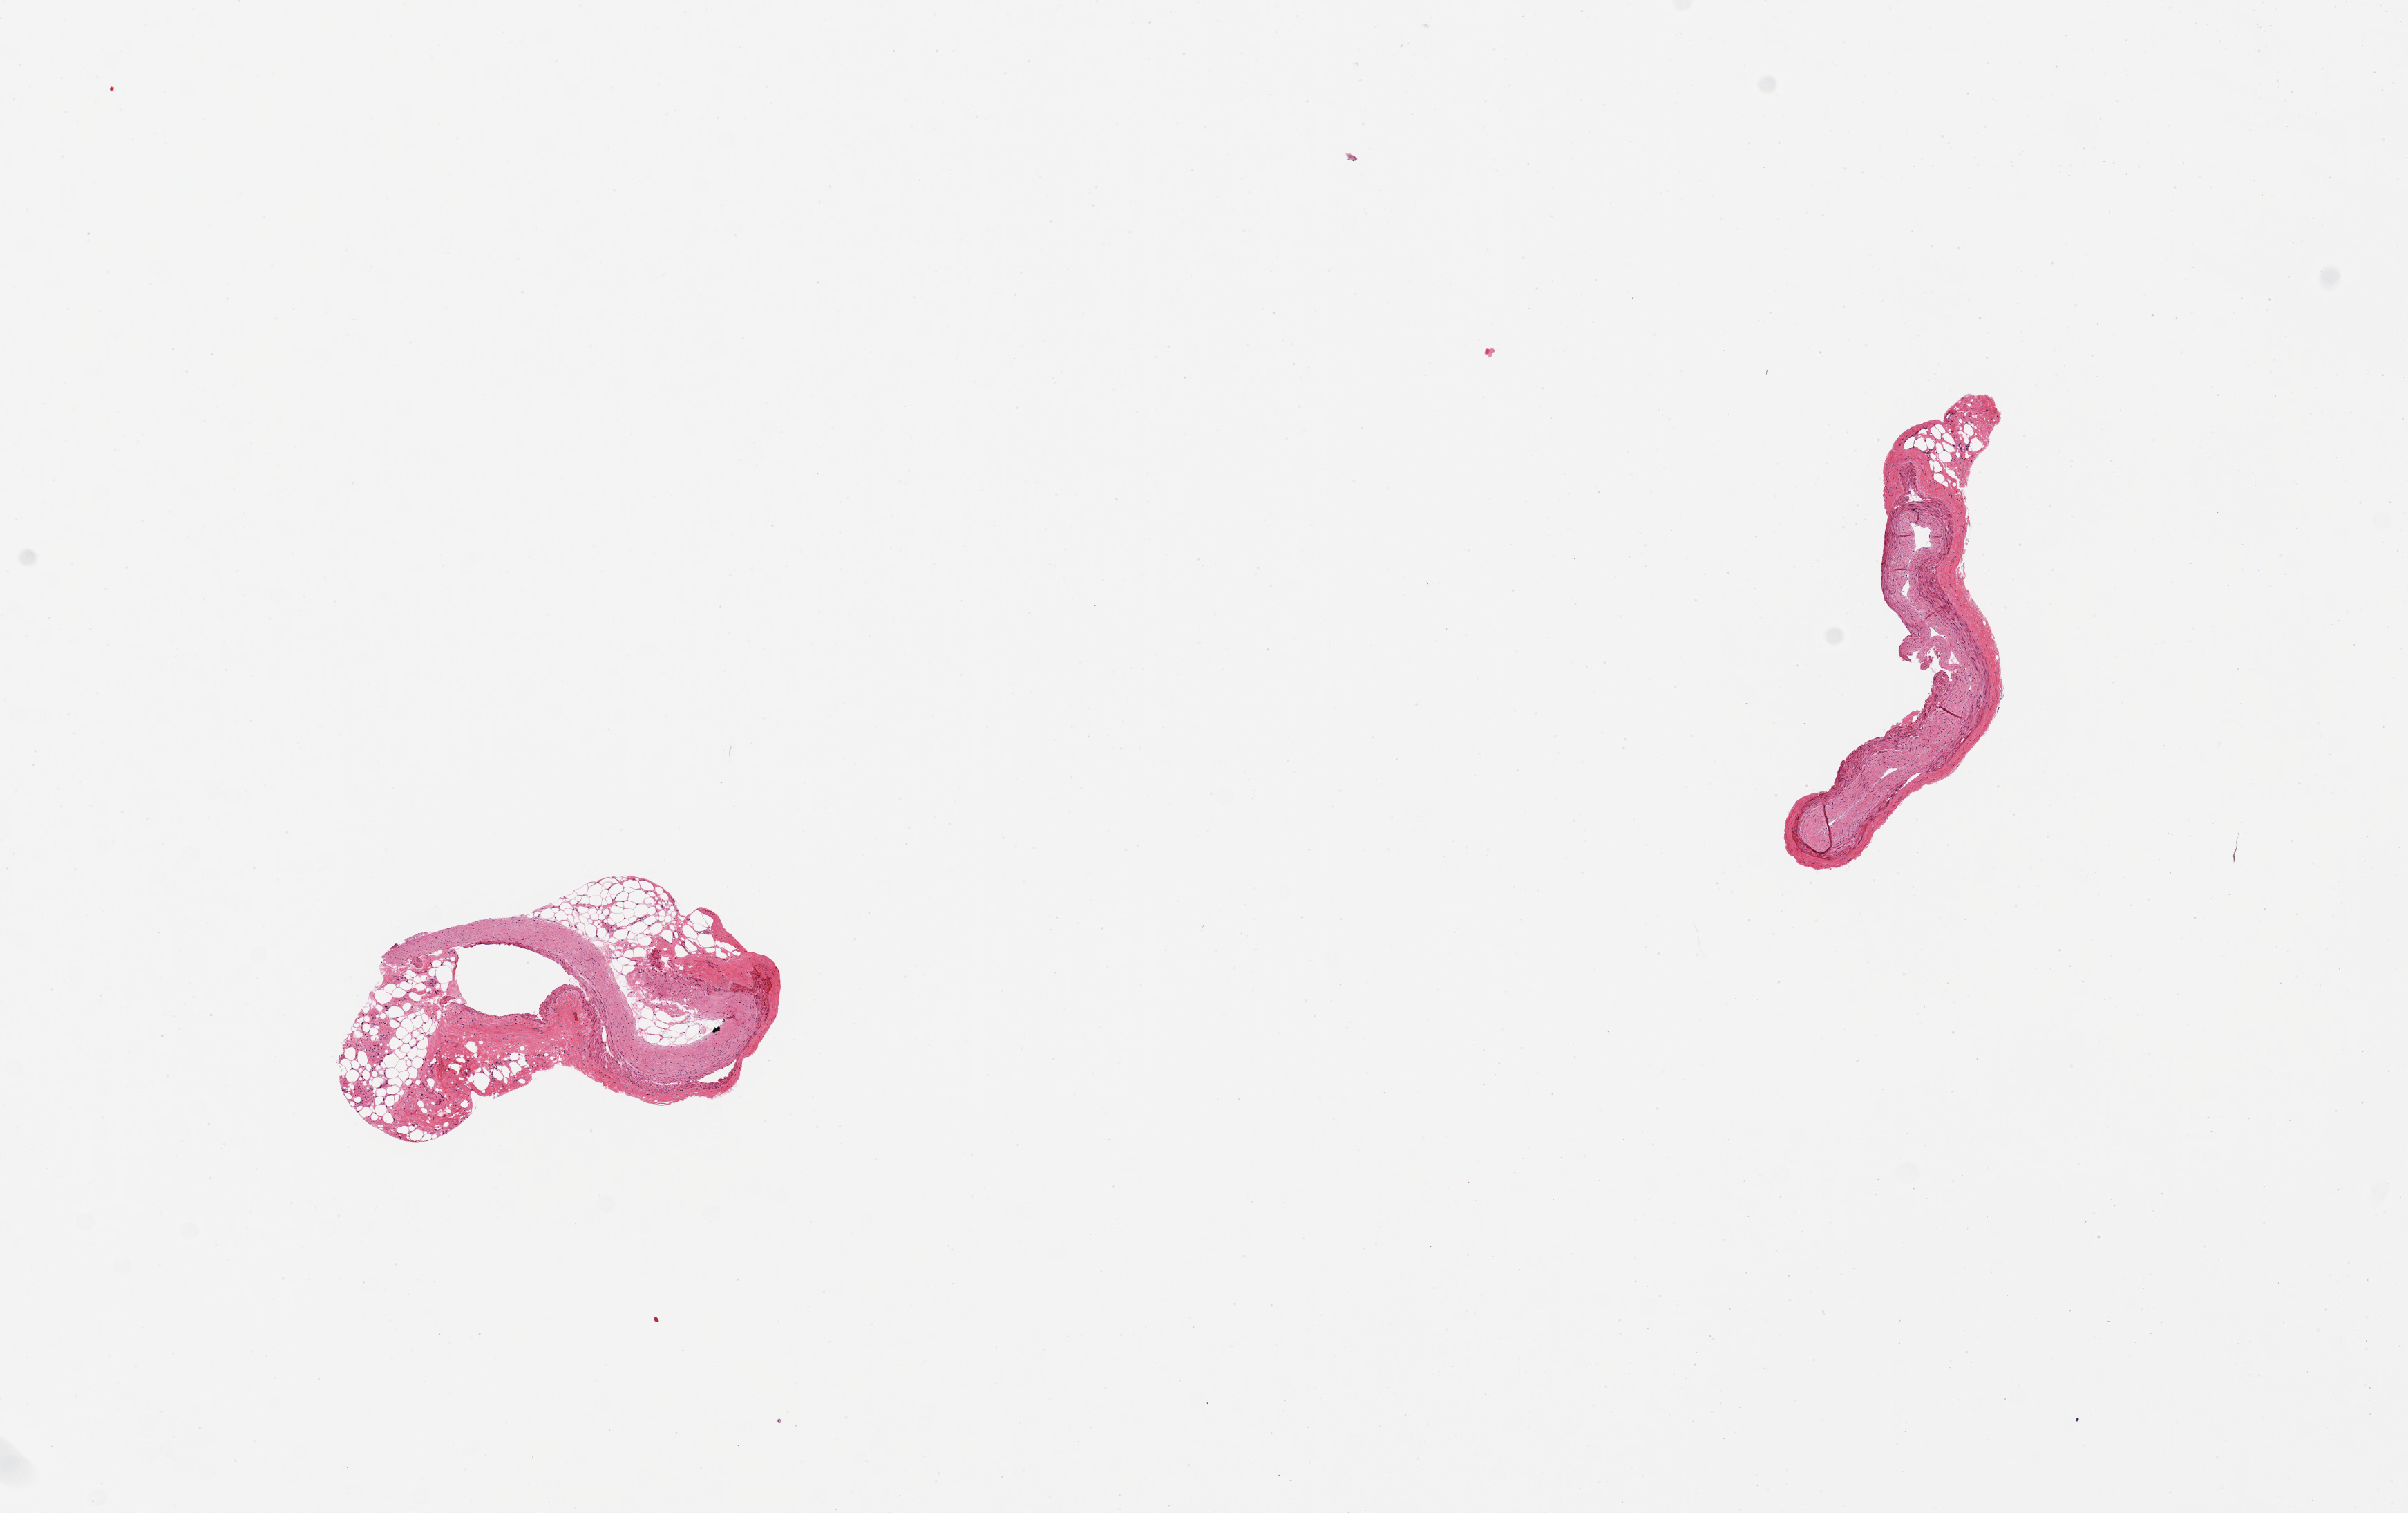
Digitized H&E-stained section, whole scanned area (about 13.8 x 8.7 mm) shown as a low-resolution overview, PAXgene-fixed, paraffin-embedded tissue, target tissue: coronary artery, tissue donor sample. Donor sex: male.
* reviewer comment on this tissue sample: 2 pieces, not artery, unknown